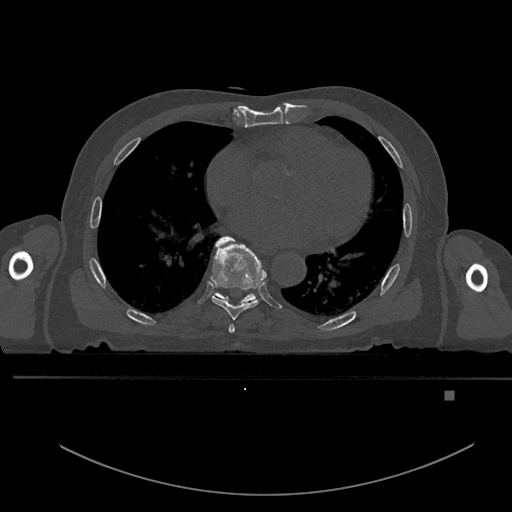
CT including the spine, one axial slice. Slice 240 of 969 in the series (ordered by position). Bone window (W 1800 / L 400 HU). 0.5 mm slice thickness. 512 × 512 image matrix, field of view 456 × 456 mm. Patient: male, 82 years. From the clinical record (not read from this slice): primary cancer: prostate; vertebrae with lytic lesions (as recorded): T11, T9, T8, T2.
Structures marked on this image (semi-automatically segmented with operator editing):
- T6 vertebra: bounding box [x1, y1, x2, y2] px = [228, 324, 235, 333]
- T7 vertebra: [211, 236, 267, 320]
- T8 vertebra: [211, 291, 256, 304]